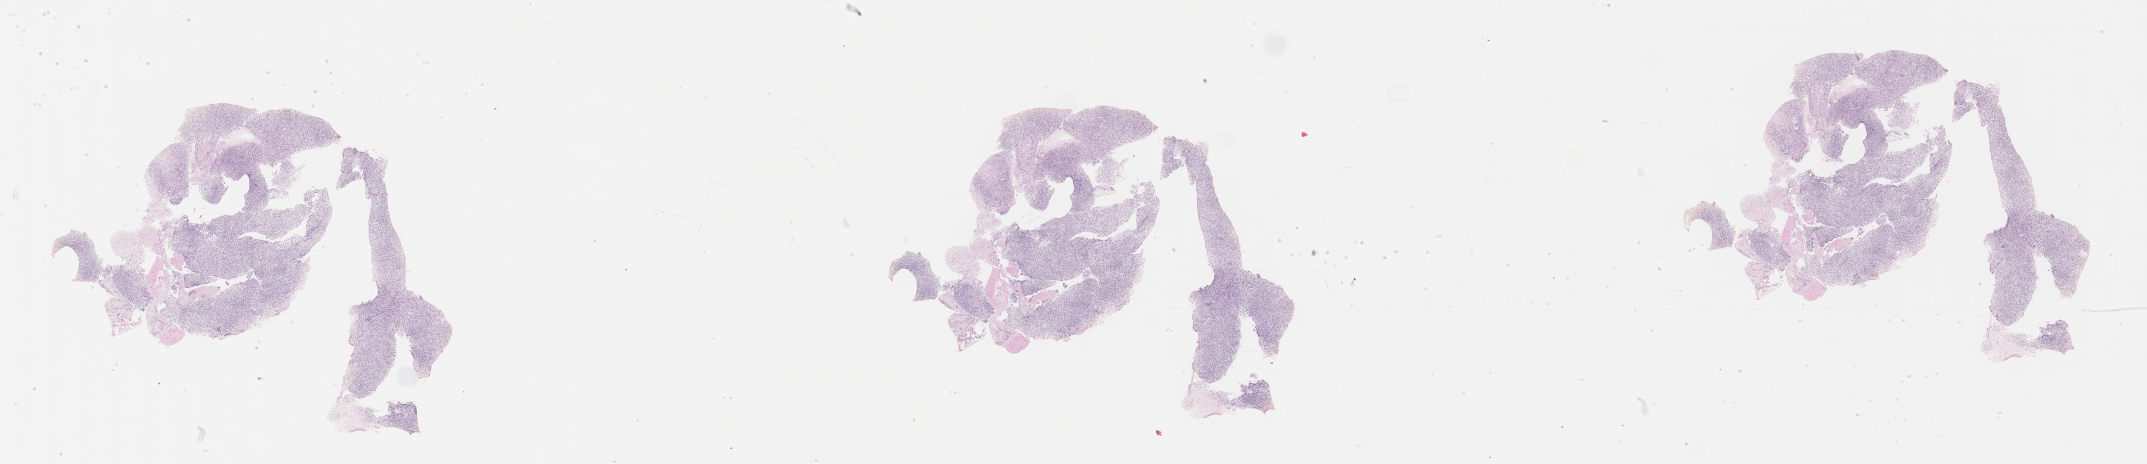
Whole-slide image, haematoxylin and eosin stain of tumor tissue — whole scanned area (about 34.7 x 7.5 mm) shown as a low-resolution overview, formalin-fixed, paraffin-embedded (FFPE) tissue, site: soft tissue, pelvis. Patient: male, age 1.6 years at diagnosis.
• primary site (case record): prostate
• metastatic status at presentation (as recorded): non-metastatic
• diagnosis: rhabdomyosarcoma; histological classification: embryonal rhabdomyosarcoma
• stage (as recorded): 3